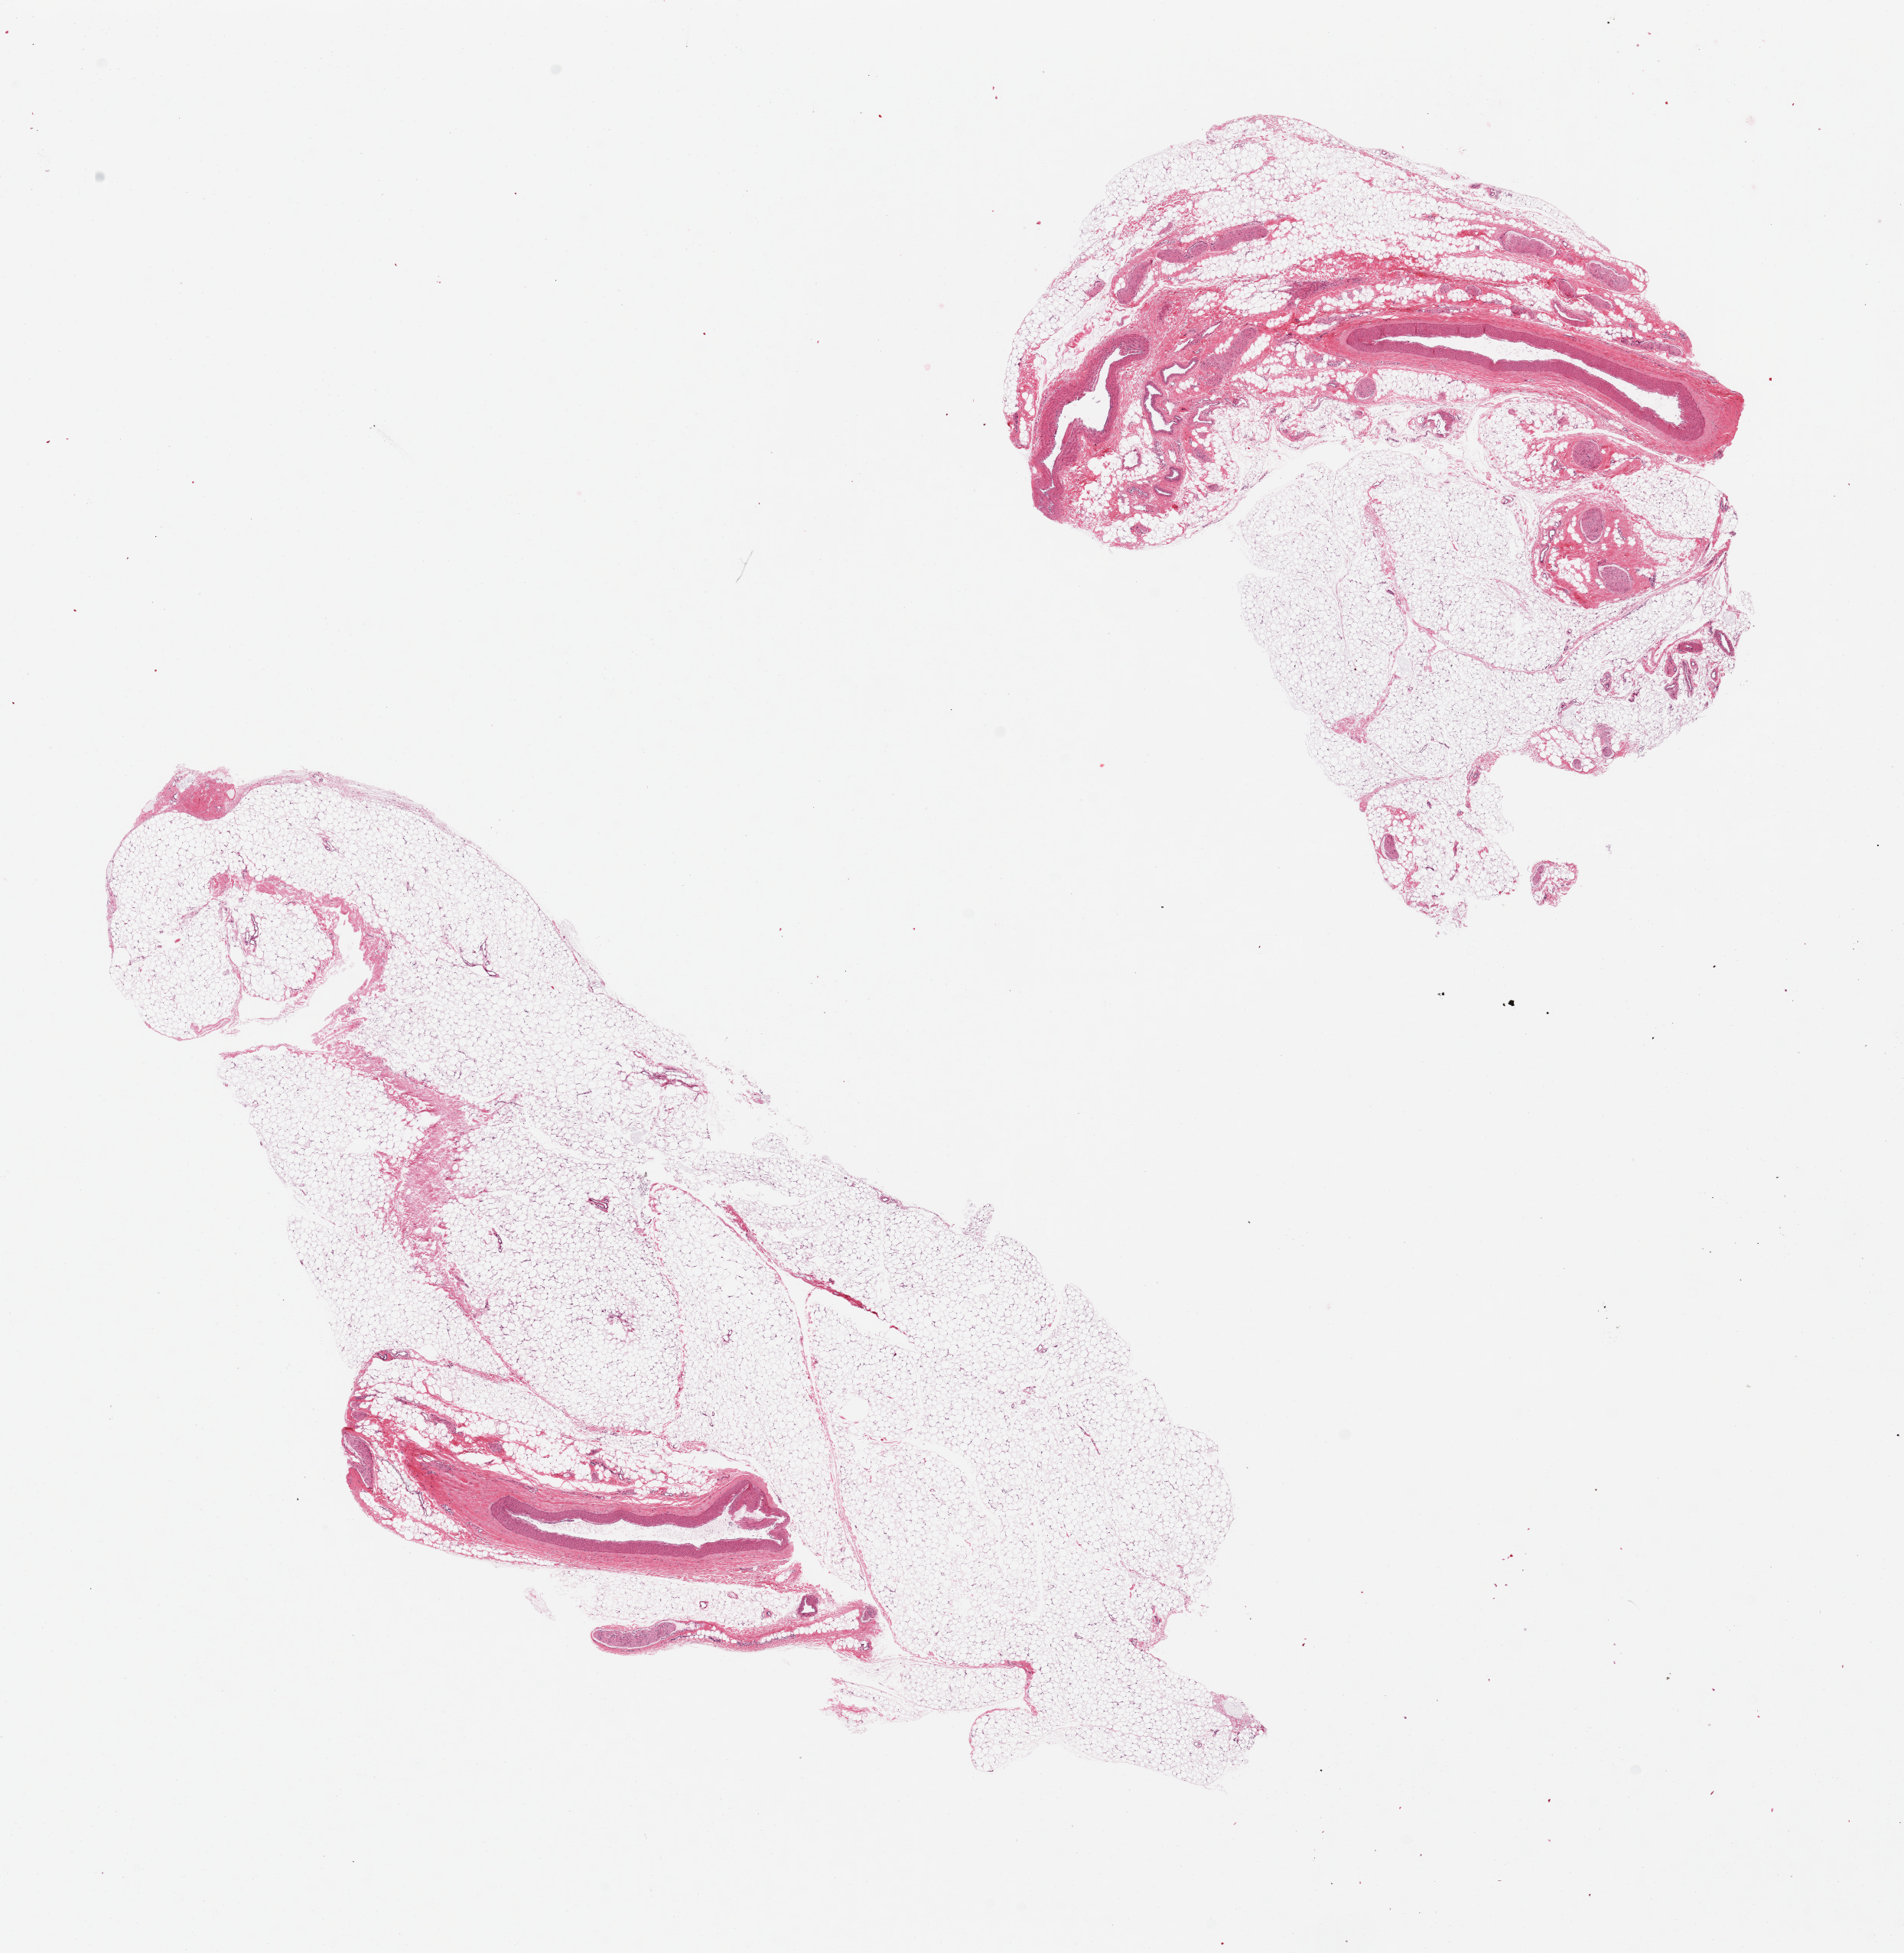
H&E whole-slide image, brightfield, low-resolution overview of the scanned area, about 19.7 x 20.2 mm (from a 20x scan); PAXgene-fixed paraffin-embedded (PFPE) section; target tissue: omentum; tissue donor sample. Donor: female.
* reviewer comment on this tissue sample: 2 pieces, includes several prominent vessels and nerve